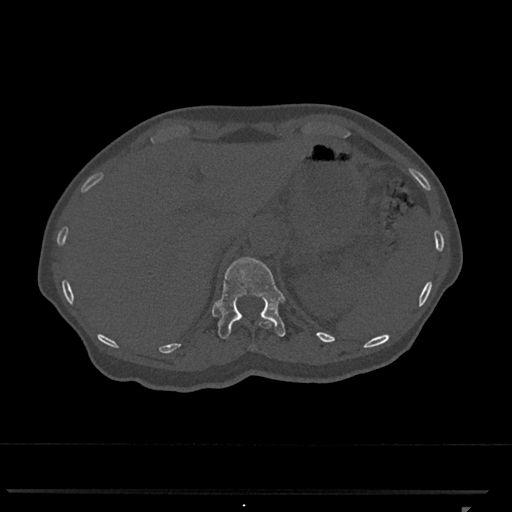
CT including the spine, one axial slice. Slice 477 of 793 in the series (ordered by position). 120 kVp. Bone window (W 1800 / L 400 HU). 512 × 512 image matrix. Female patient, age 62 years. Case-level facts recorded for this patient, not image findings: primary cancer: renal.
Annotated regions visible in this slice (semi-automatic segmentation, software-assisted and operator-edited):
- T11 vertebra: bounding box <259,321,272,329> (left, top, right, bottom; pixels)
- T12 vertebra: <215,257,286,339>